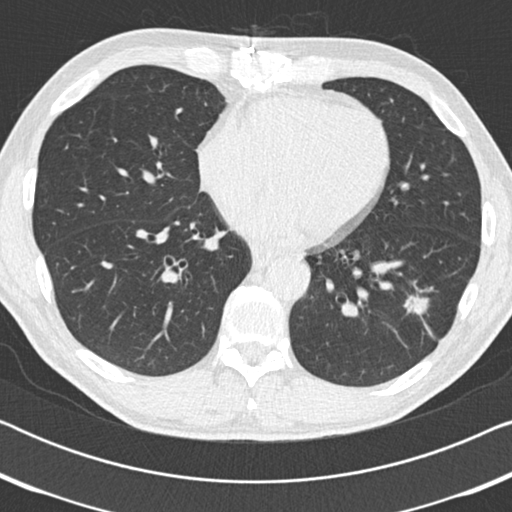
Axial slice from a low-dose chest CT screening exam, third annual screen, lung window (W 1500 / L -600 HU), 2 mm slice thickness, standard (soft-tissue) reconstruction kernel (B30f), 120 kVp, slice 112 of 186 in the series. Male participant, aged 59 years at enrolment. Current smoker at enrolment.
- Expert-annotated lung lesion, bounding box (x1, y1, x2, y2) in pixels: (389, 278, 456, 341).
- The screening reader recorded 2 non-calcified nodules or masses ≥4 mm on this exam (left lower lobe, right middle lobe); which of them this box marks is not recorded.
- Official screen result: positive, other.
- Later outcome: lung cancer diagnosed 73 days after this screen — adenocarcinoma, NOS, left lower lobe, poorly differentiated (G3), stage IA (AJCC 6th edition), 20 mm at pathology.